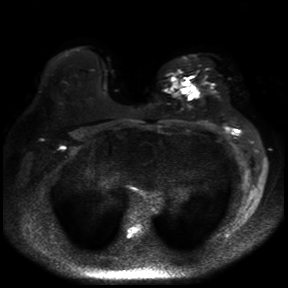
Breast MRI, one axial slice; slice 23 of 30 in the series (ordered by position); diffusion-weighted series; image 2 of 4 stored at this slice position (different b-values; order by instance number); 3 T; 288 × 288 image matrix, field of view 360 × 360 mm. Female patient.
Annotated regions visible in this slice (manually delineated by an expert):
- tumour on diffusion-weighted imaging: bounding box (x1, y1, x2, y2) in pixels: (180, 81, 198, 99)